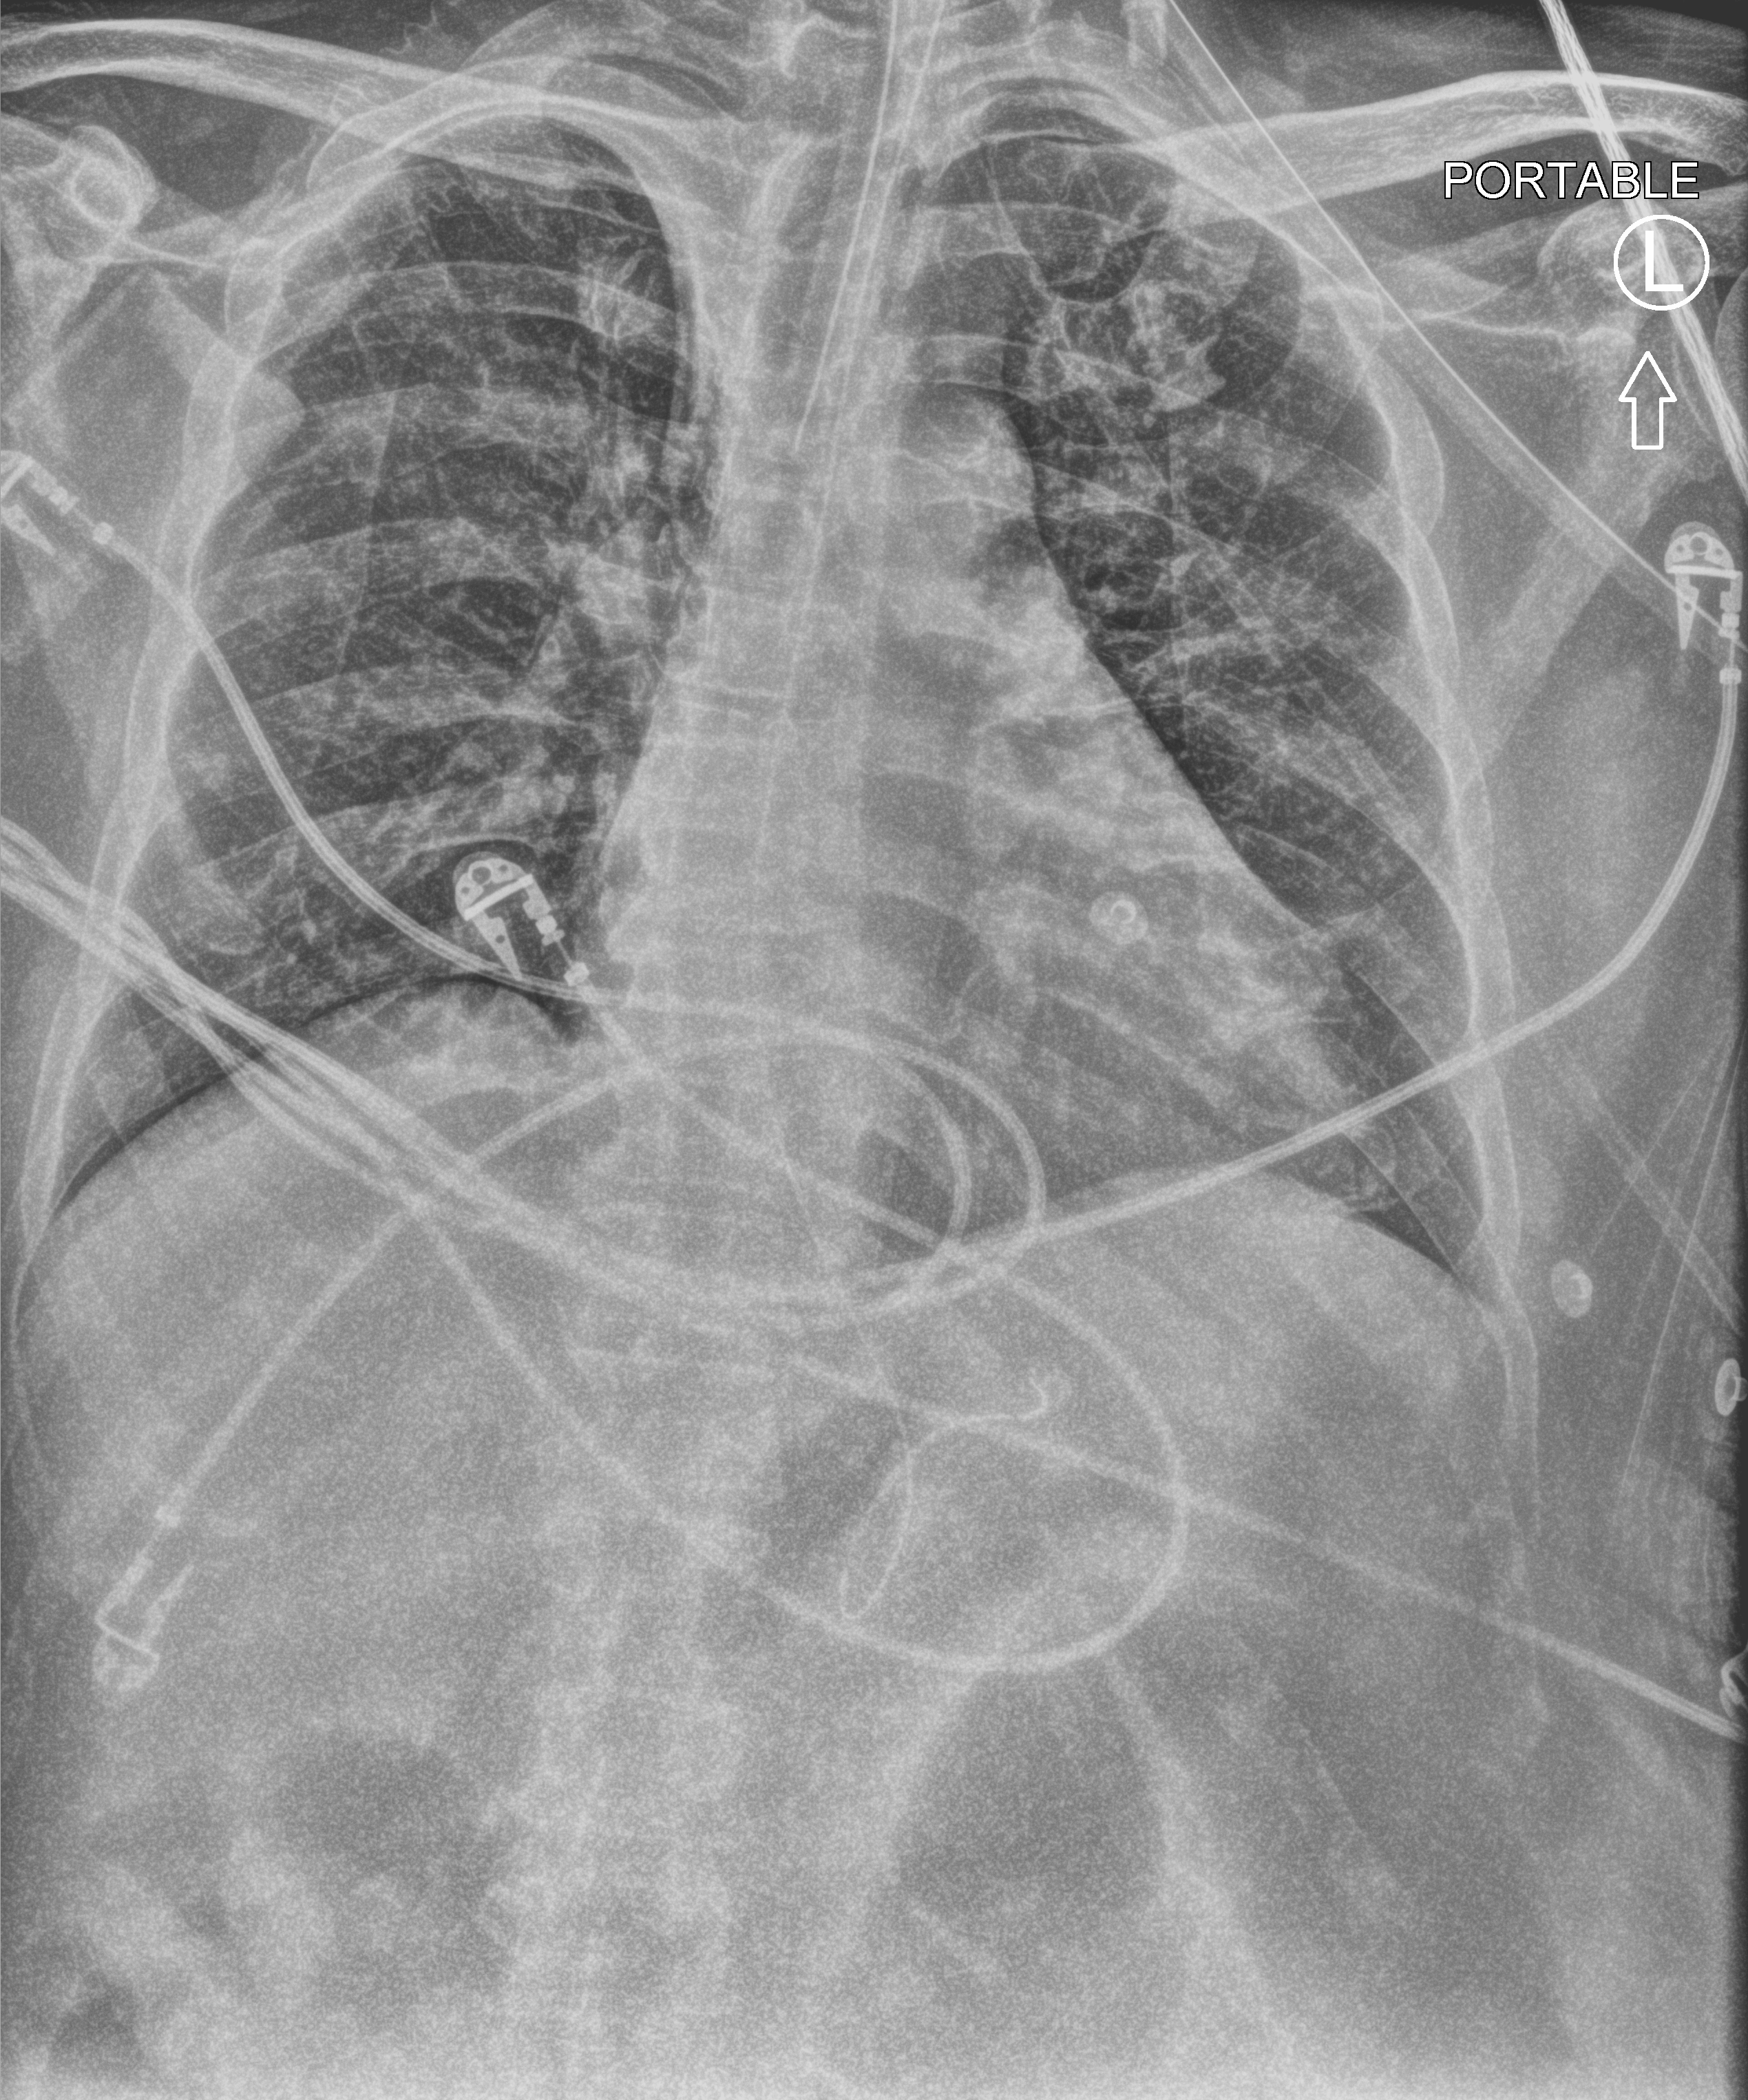
Bedside chest radiograph (computed radiography), anteroposterior (AP) projection. Patient hospitalised with COVID-19, aged 18–59 years.
From the hospital-stay record, not from the radiograph (when in the stay this image was taken is not recorded): length of hospital stay: 37 days; COPD (admission record): no.